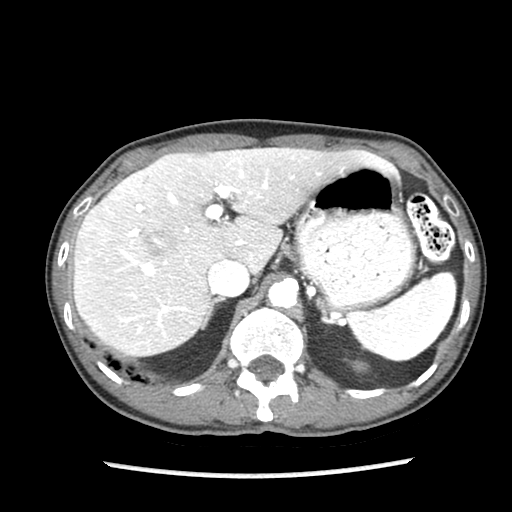
Contrast-enhanced abdominal CT (liver protocol), one axial slice. Position 59 of 87 along the scan axis. Reconstruction kernel STANDARD. 140 kVp. Soft-tissue window (W 400 / L 40 HU). 2.5 mm slice thickness. 512 × 512 image matrix, field of view 300 × 300 mm. Case-level facts recorded for this patient, not image findings: diagnosis: hepatocellular carcinoma (patient treated with transarterial chemoembolisation; whether this scan precedes or follows treatment is not stated here); TNM stage (as recorded): Stage-IIIB.
Structures marked on this image (semi-automatically segmented with operator editing):
- liver parenchyma outside the tumour (the mass and vessels are separate outlines, so this box may not span the whole liver): box from (x=74, y=148) to (x=376, y=356) px
- mass: (x=147, y=234)–(x=173, y=259)
- liver vessels: (x=120, y=170)–(x=268, y=332)